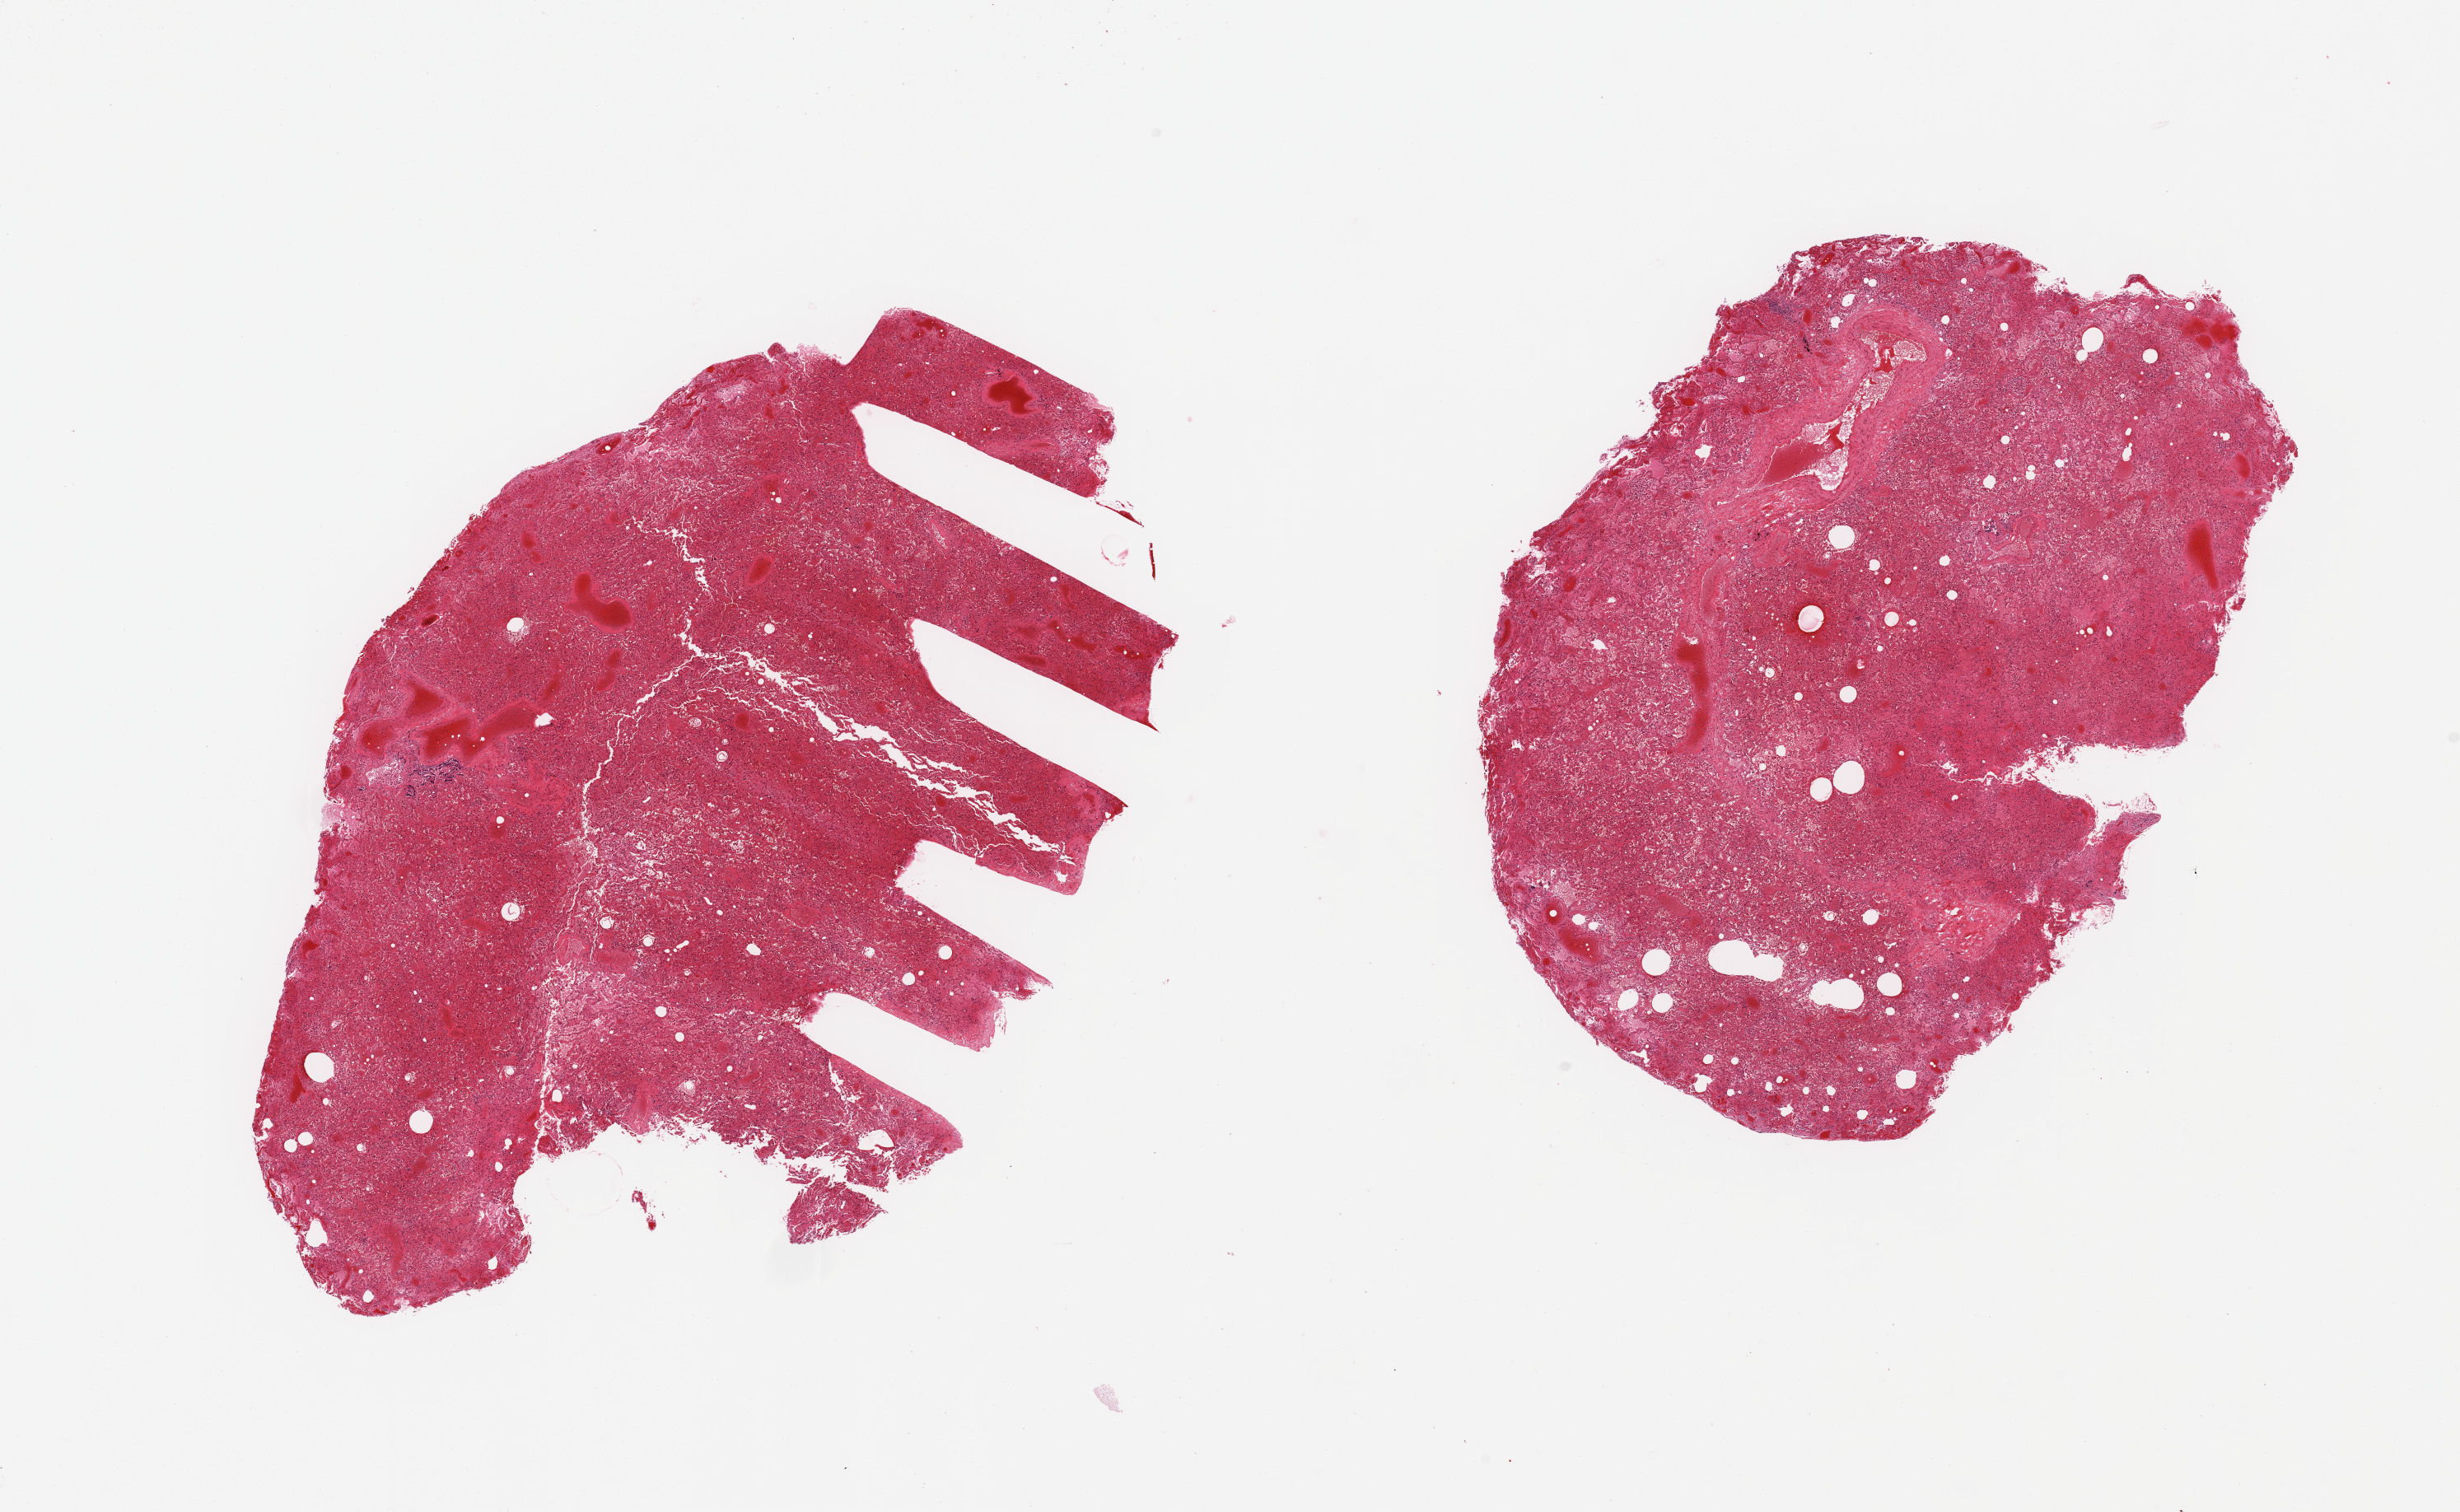
H&E whole-slide image — a low-resolution overview of the entire scanned area, about 23.6 x 14.5 mm (slide scanned at 20x); PAXgene-fixed, paraffin-embedded tissue; sampled site (target tissue): lung; donor tissue sample. Donor: male.
Pathologist's review note for this sample: 2 pieces; marked congestion.